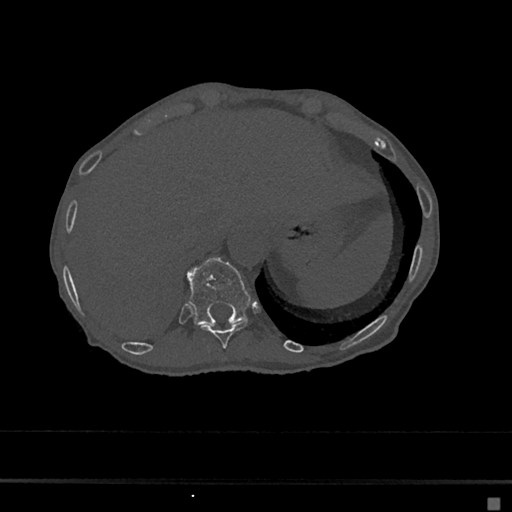
CT including the spine, one axial slice. Position 196 of 797 along the scan axis. Reconstruction kernel Br40s/3. 120 kVp. Bone window (W 1800 / L 400 HU). 0.5 mm slice thickness. 512 × 512 image matrix, field of view 360 × 360 mm. Female patient, age 68 years. Case-level facts recorded for this patient, not image findings: primary cancer: renal.
Outlined on this slice (semi-automatically segmented with operator editing):
- T10 vertebra: bounding box [x1, y1, x2, y2] px = [199, 321, 248, 348]
- T11 vertebra: [188, 258, 251, 325]